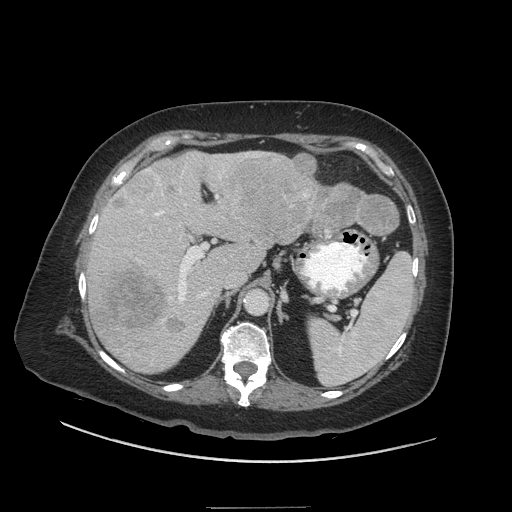
Contrast-enhanced abdominal CT (liver protocol), one axial slice. Position 30 of 81 along the scan axis. Soft-tissue window (W 400 / L 40 HU). 2.5 mm slice thickness. 512 × 512 image matrix. From the clinical record (not read from this slice): diagnosis: hepatocellular carcinoma (patient treated with transarterial chemoembolisation; whether this scan precedes or follows treatment is not stated here); TNM stage (as recorded): Stage-II; Child-Pugh class: A; tumour nodularity: multinodular.
Structures marked on this image (semi-automatic segmentation, software-assisted and operator-edited):
- liver parenchyma outside the tumour (the mass and vessels are separate outlines, so this box may not span the whole liver): box from (x=86, y=150) to (x=349, y=372) px
- mass: (x=93, y=153)–(x=400, y=339)
- liver vessels: (x=105, y=161)–(x=225, y=303)